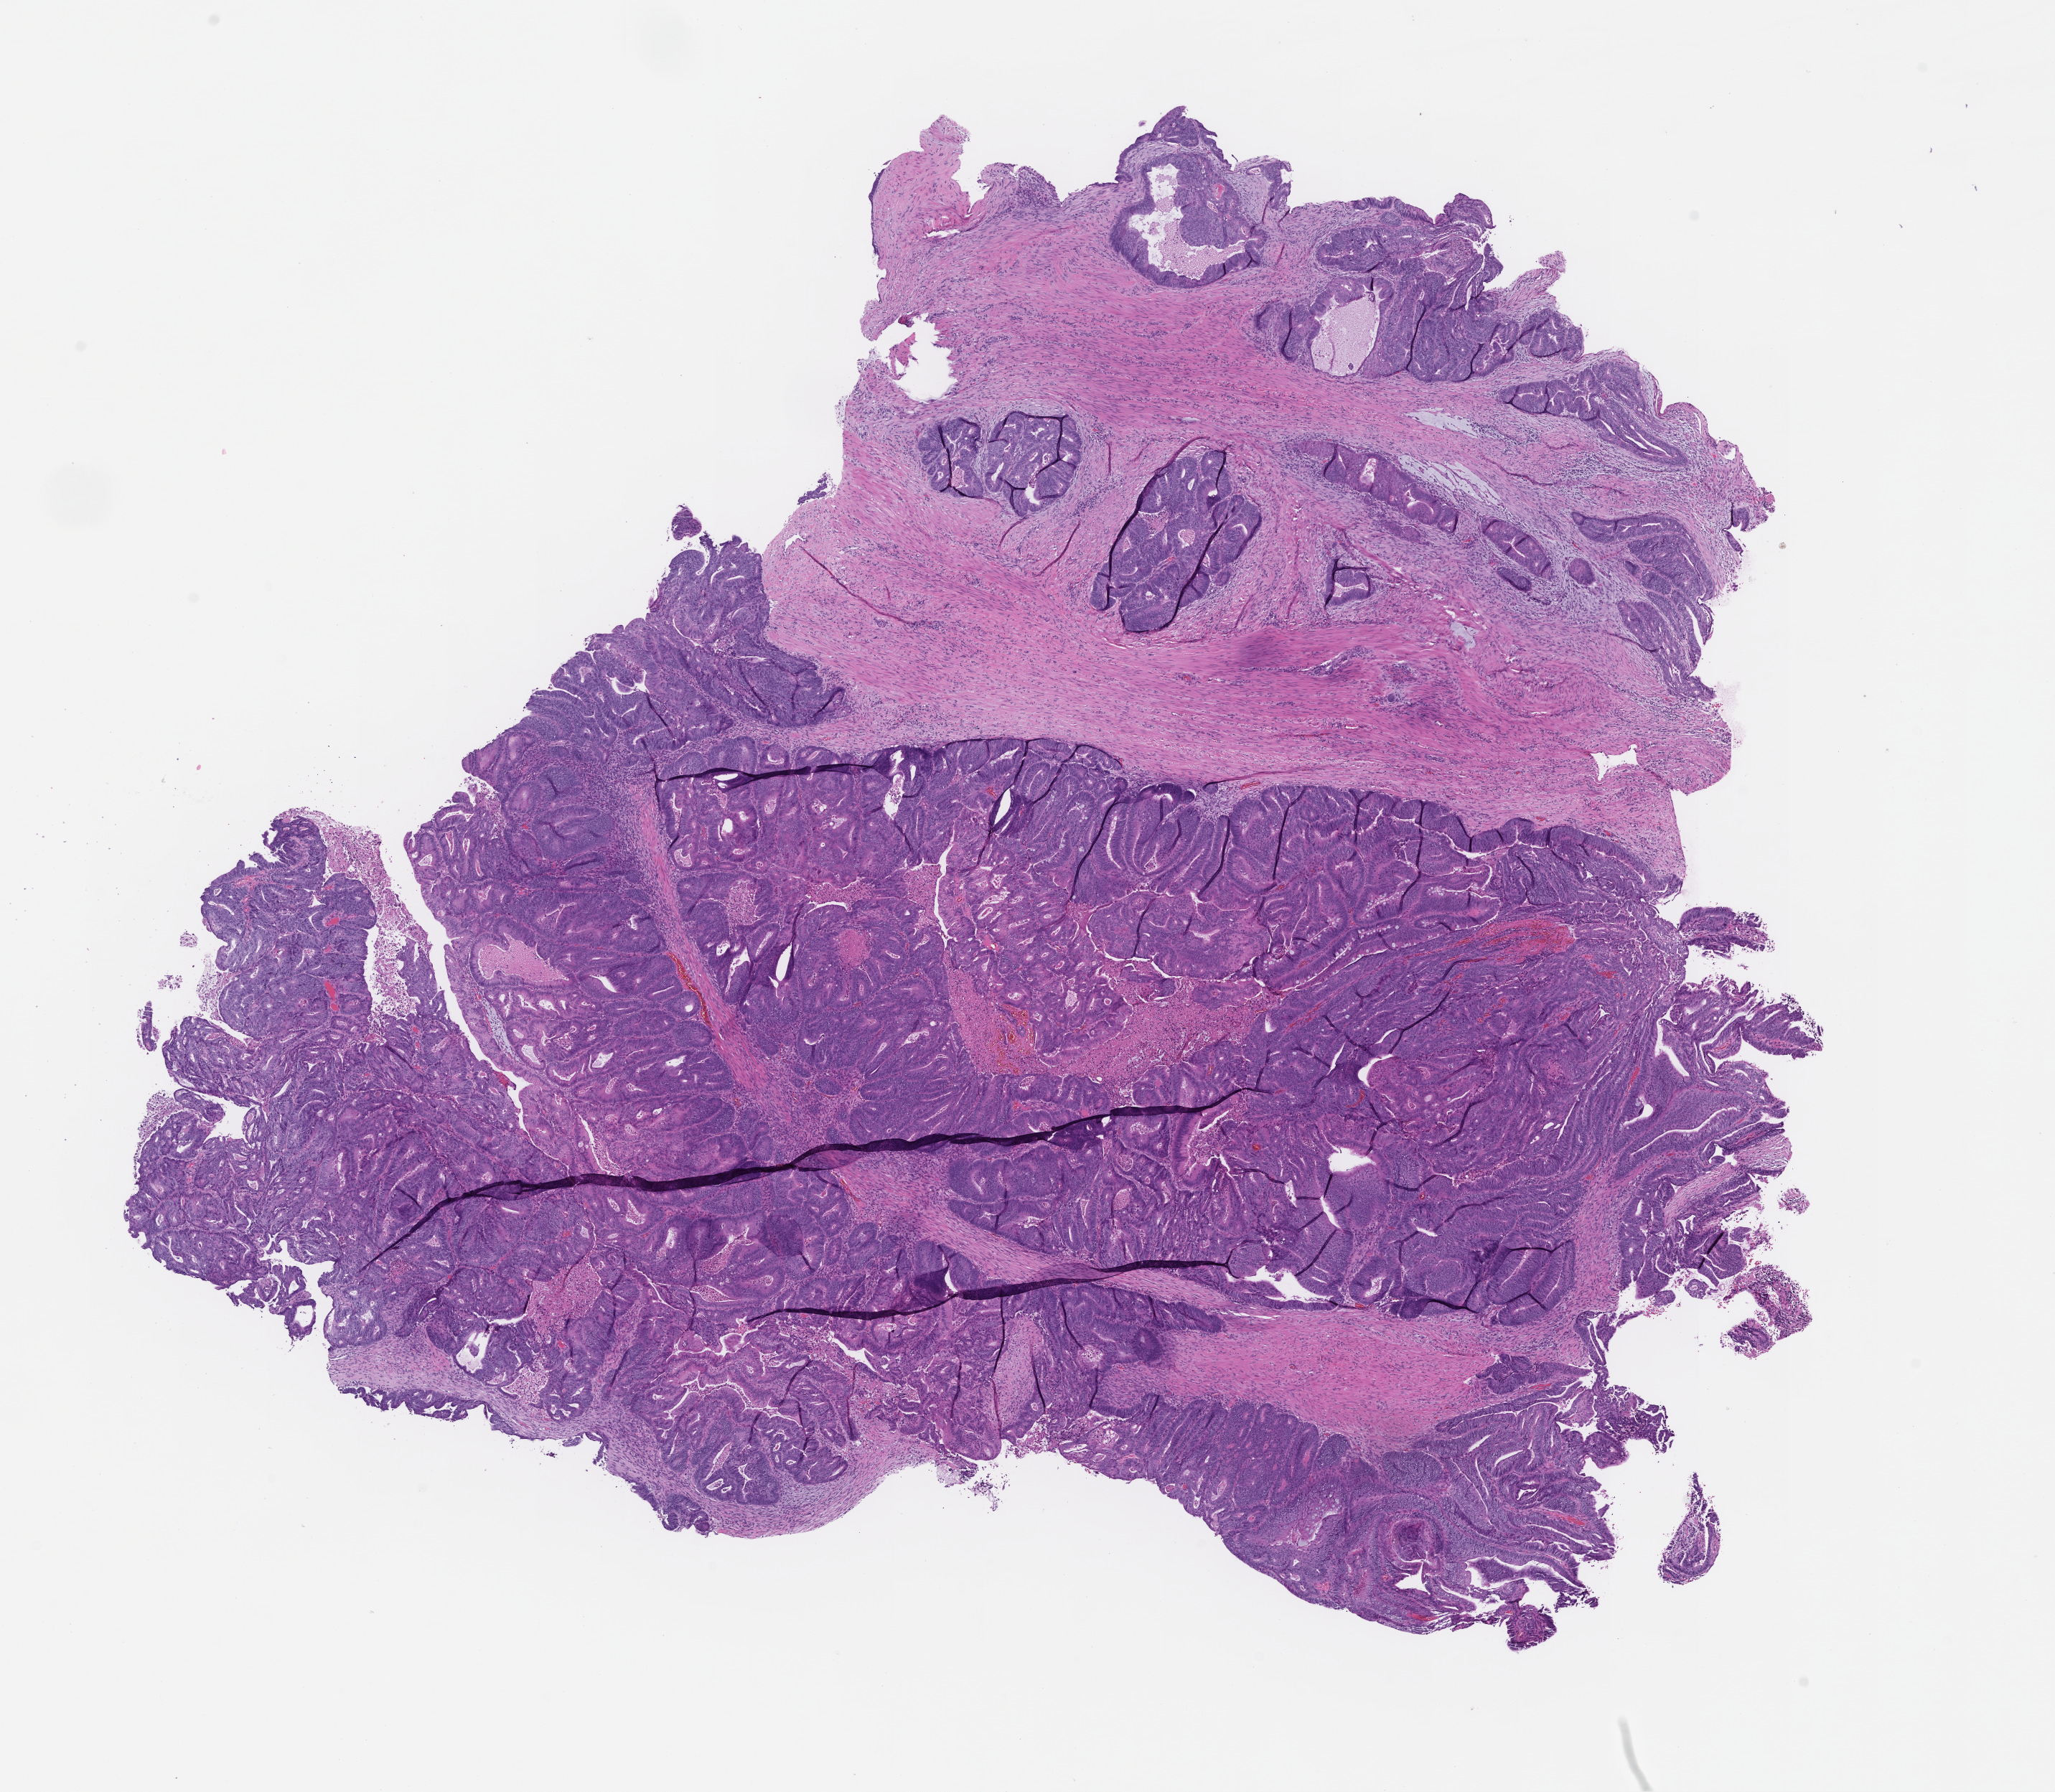
Whole-slide image, hematoxylin and eosin (H&E) stain, a low-resolution overview of the entire scanned area, about 11.6 x 10.1 mm, FFPE section, tissue site: colon, specimen time point: collected at baseline (before treatment). Patient: male.
* this section: primary tumor
* diagnosis: Colorectal Carcinoma